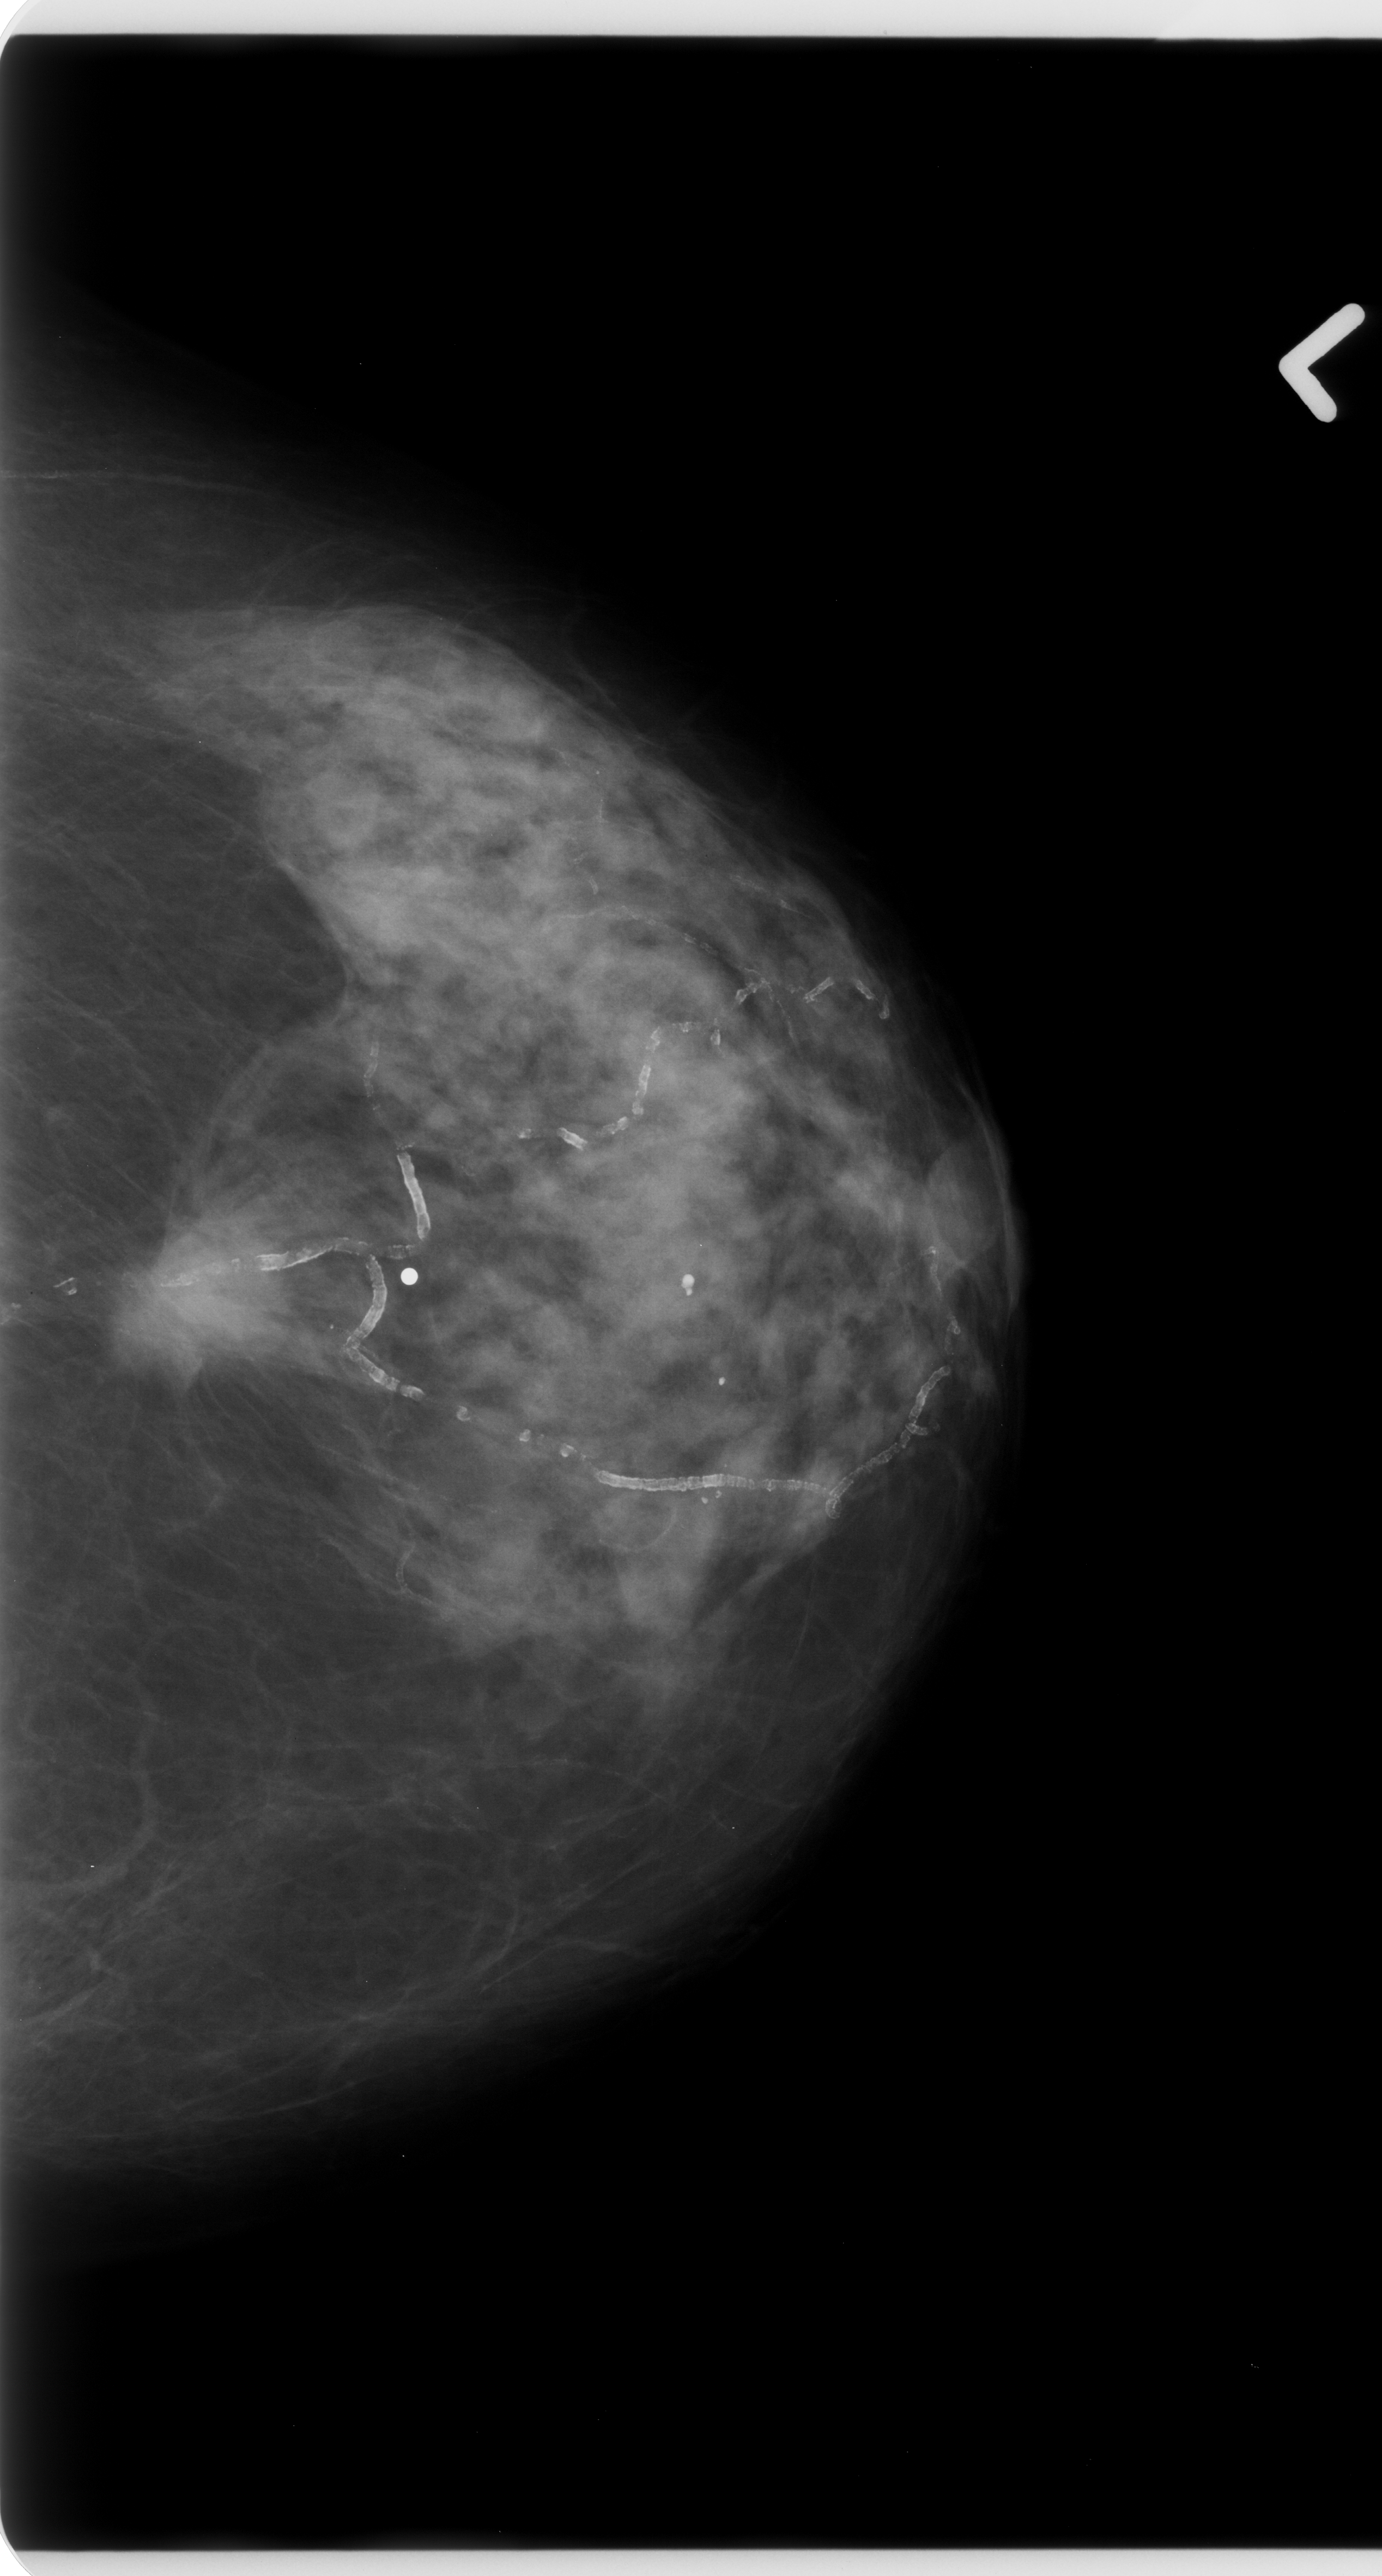
Scanned film-screen mammogram; left breast; craniocaudal (CC) view.
Abnormality record for this image: mass, shape oval, margins spiculated; BI-RADS assessment category 5; pathology (as recorded): malignant.